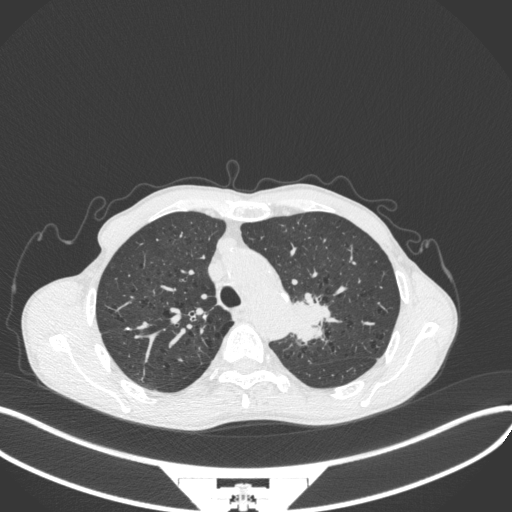
Chest CT, one axial slice; position 312 of 394 along the scan axis; 120 kVp; lung window (W 1500 / L -600 HU); 1 mm slice thickness; 512 × 512 image matrix, field of view 400 × 400 mm. Patient: male, 65 years. From the clinical record (not read from this slice): clinical TNM (as recorded): T2b N0 M0; histopathological grade: G2.
Structures marked on this image (bounding box drawn by a radiologist):
- lung tumour (recorded histology: adenocarcinoma): bounding box (x1, y1, x2, y2) in pixels: (283, 286, 339, 347)